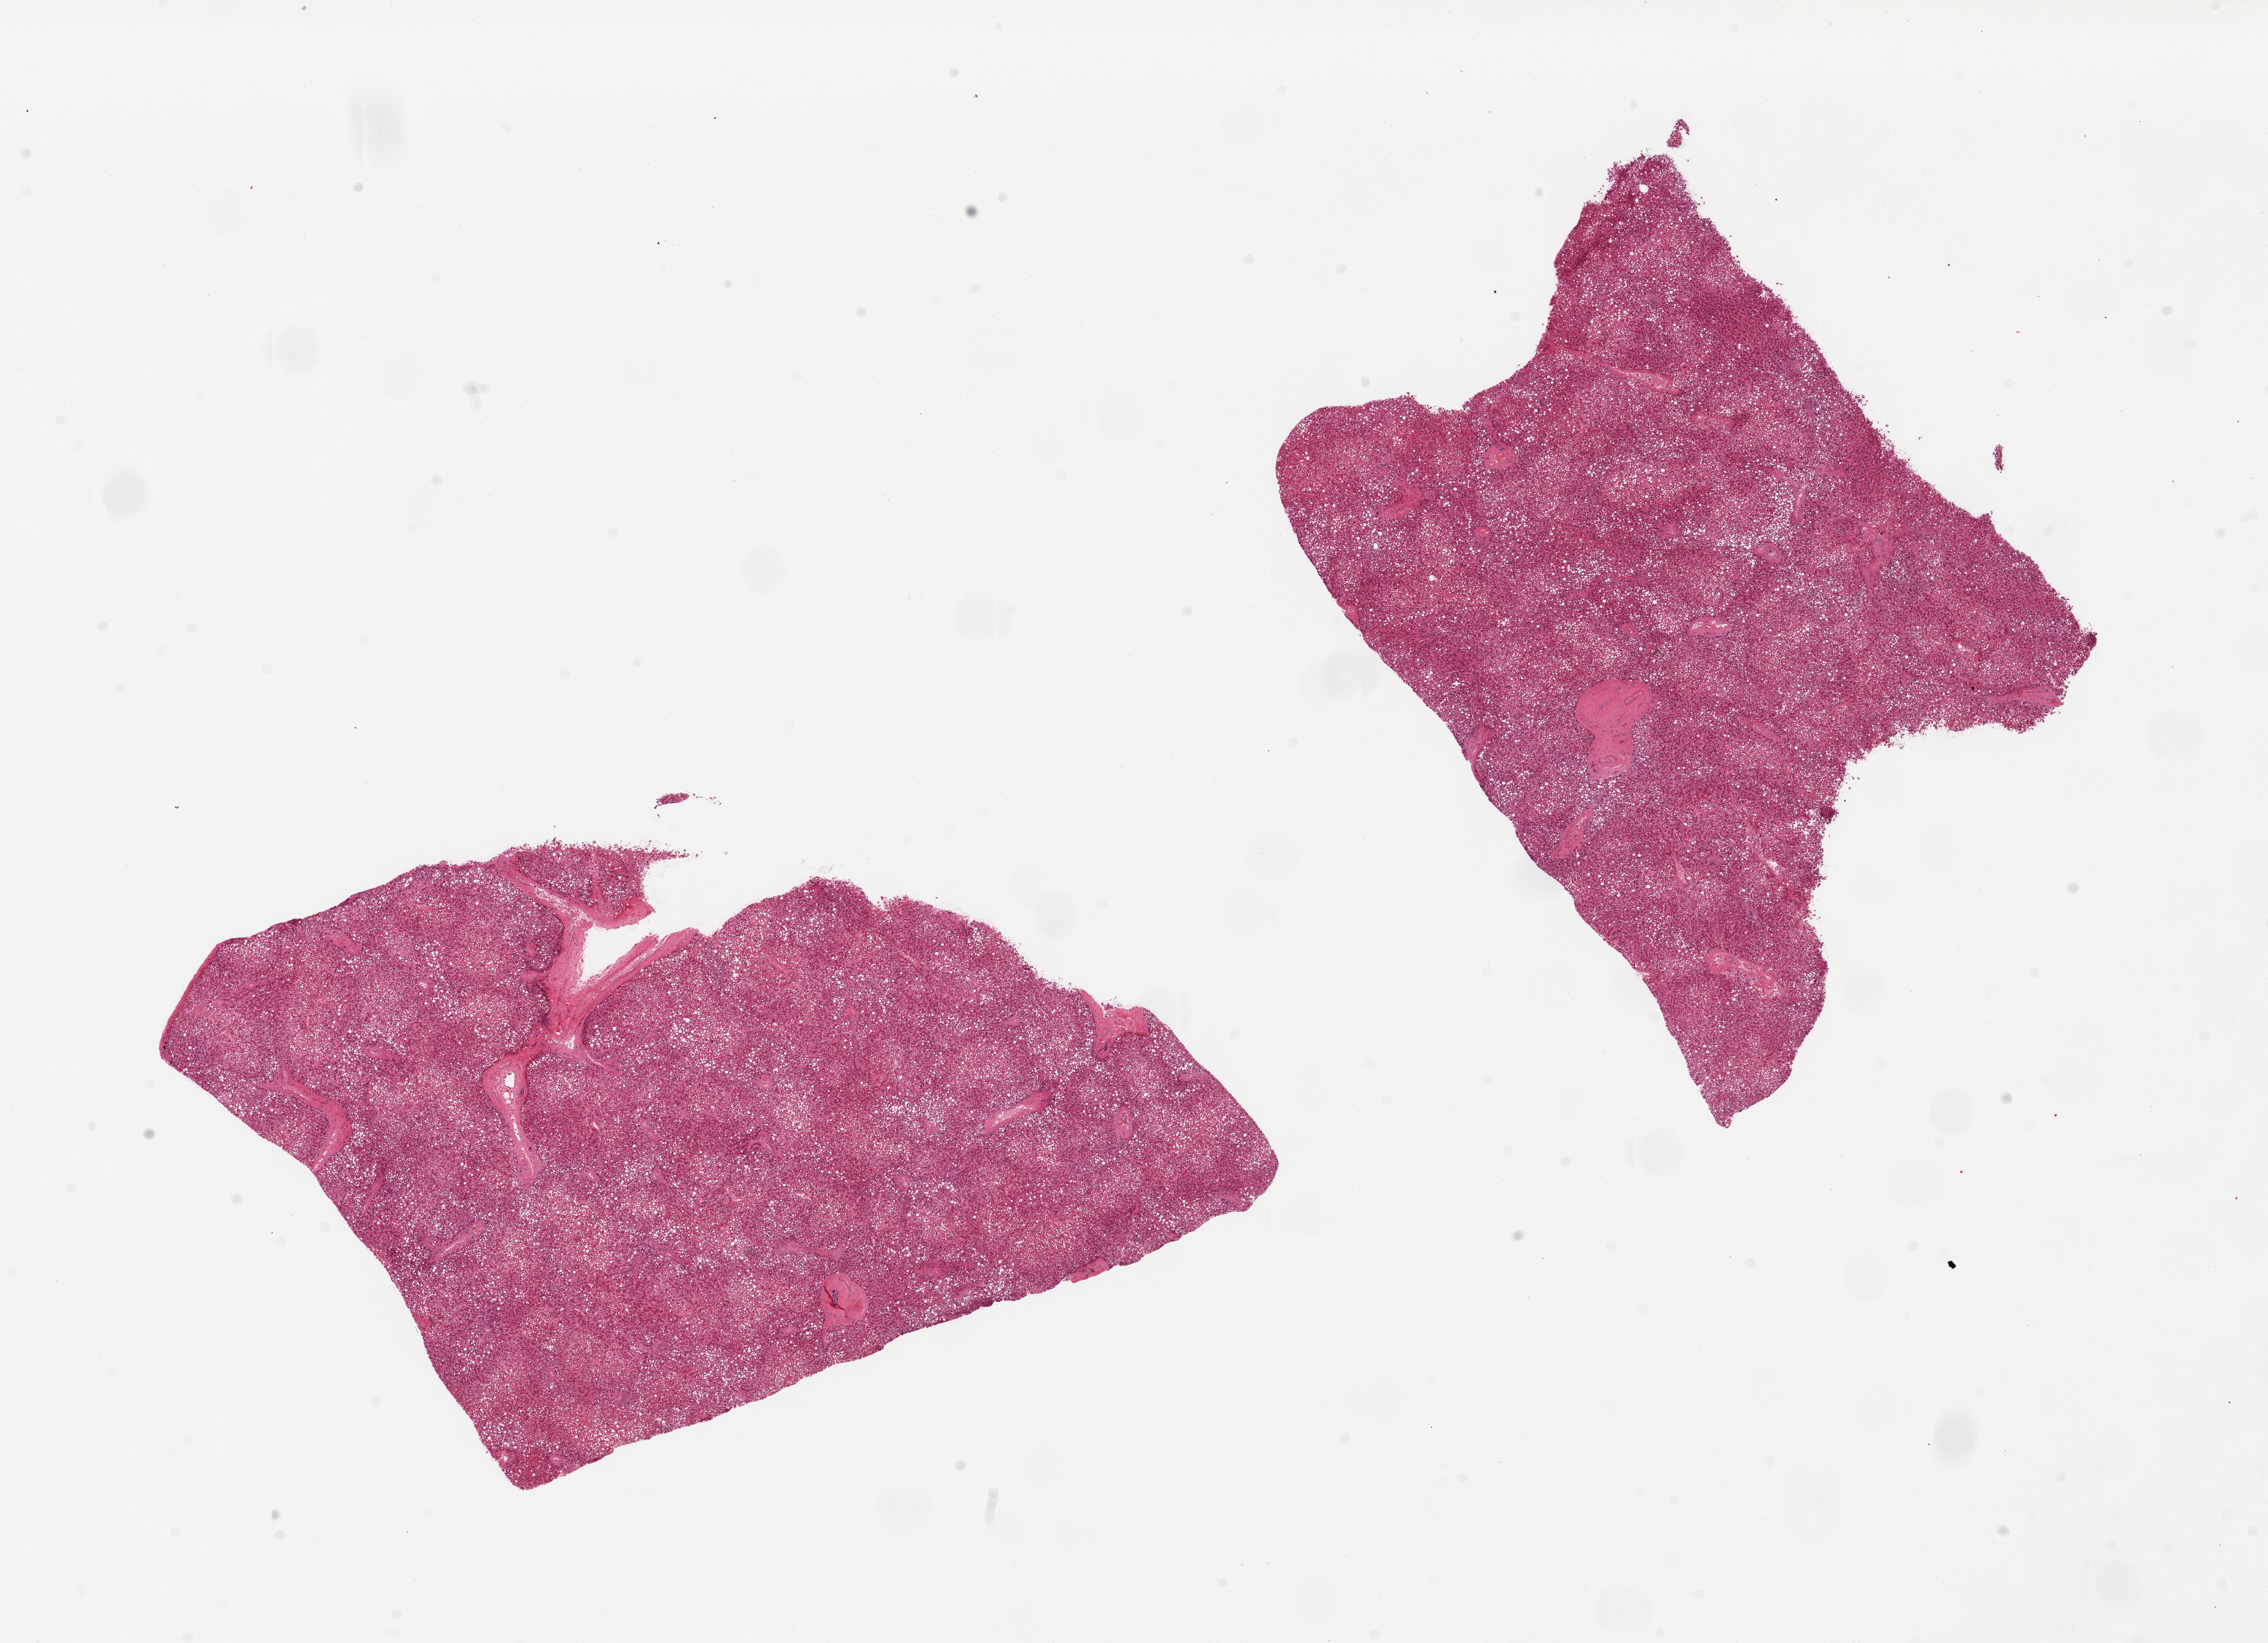
Whole-slide image, hematoxylin and eosin (H&E) stain — whole scanned area (about 24.6 x 17.8 mm, slide scanned at 20x) shown as a low-resolution overview. PAXgene-fixed, paraffin-embedded tissue. Section of liver (target tissue). Donor tissue sample. Donor sex: male.
- review note (as recorded): 2 pieces, diffuse macrovesicular steatosis involving ~60% of parenchyma